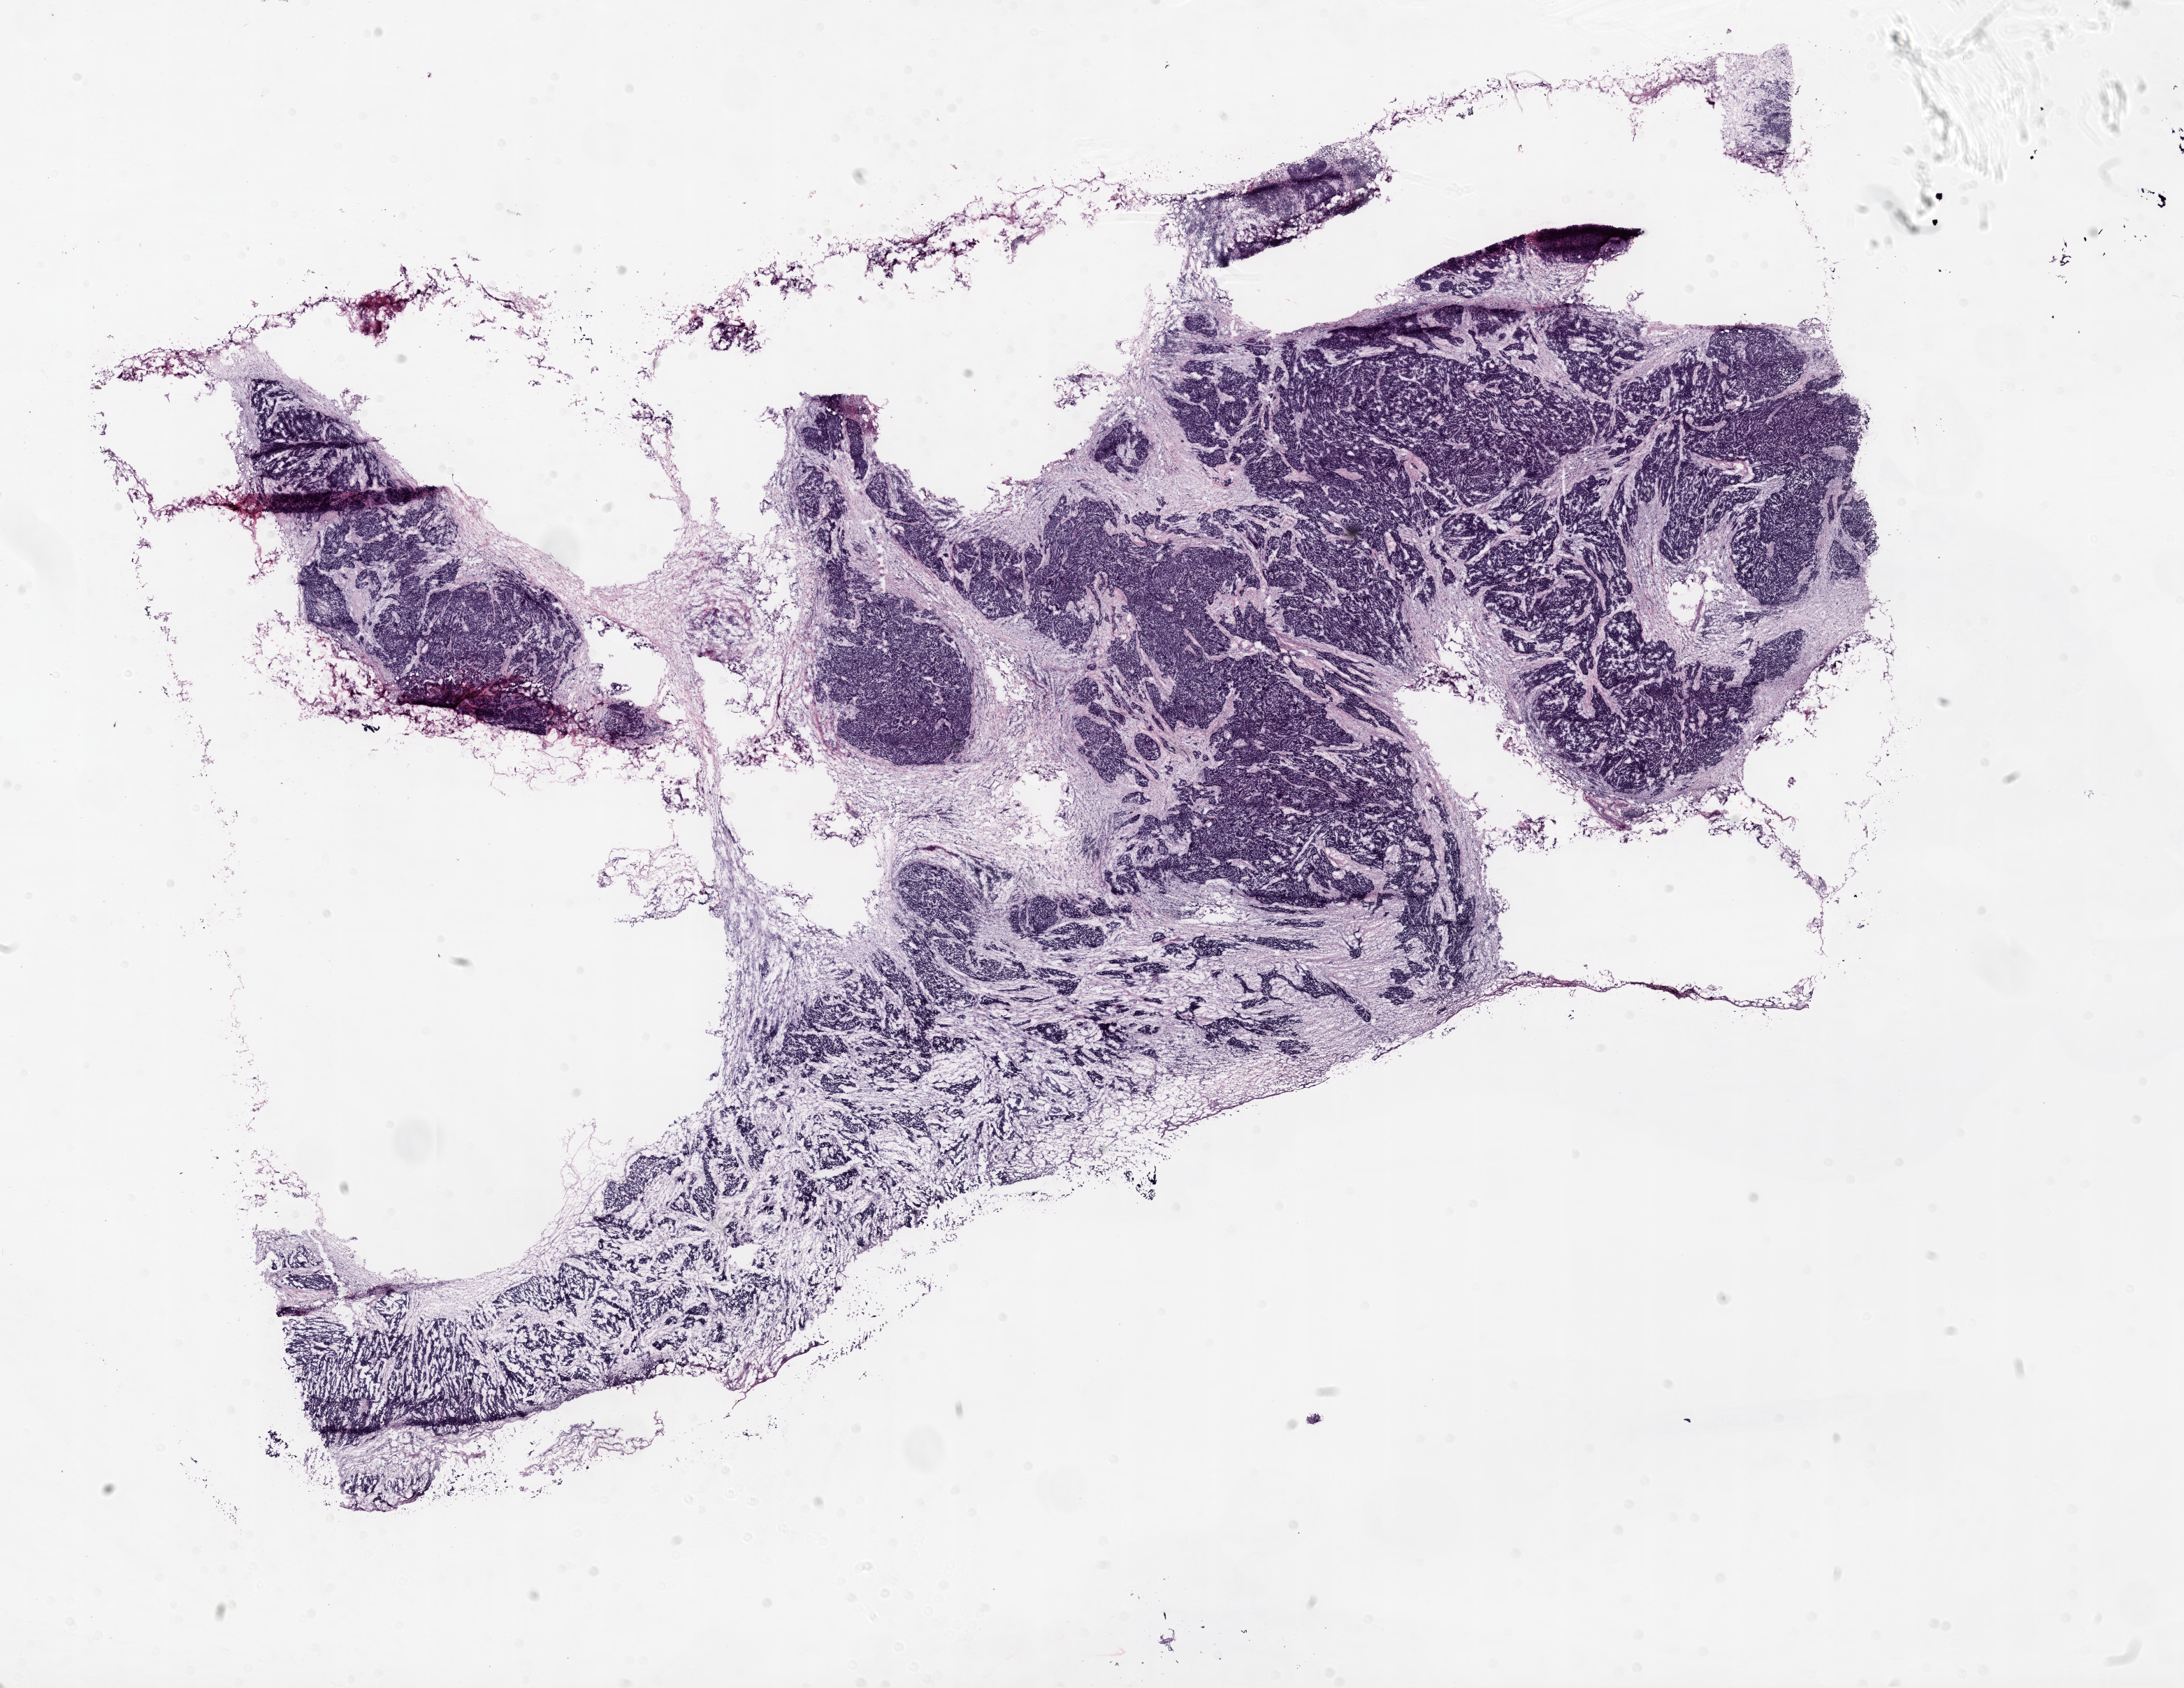
Whole-slide histology image, Hematoxylin and eosin (H&E) stained — a low-resolution overview of the entire scanned area, about 25.1 x 19.4 mm (from a 20x scan), frozen section, ovary, primary tumour sample. Patient: female, age at initial diagnosis 71 years. Histologic grade: G3 (poorly differentiated). Composition of this section per pathologist review: tumour cells 60%, tumour nuclei 90%, normal cells 0%, stromal cells 40%, necrosis 0%. Infiltration values recorded for this section: lymphocyte infiltration 5%, monocyte infiltration 0%, neutrophil infiltration 0%.
Laterality: bilateral. Histologic diagnosis: Serous cystadenocarcinoma, NOS. FIGO stage: IIIC.